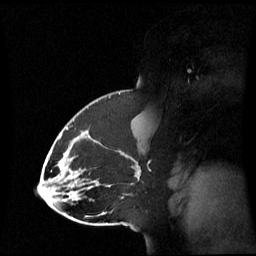
Breast MRI (dynamic contrast-enhanced), one sagittal slice; slice 38 of 60 in the series (ordered by position); dynamic contrast-enhanced series, image 2 of 3 at this slice position (ordered by acquisition); 1.5 T; TE 4.2 ms, TR 8.4 ms; 2.8 mm slice thickness; 256 × 256 image matrix, field of view 270 × 270 mm. Patient: female, 43 years. From the clinical record (not read from this slice): setting: breast cancer imaged before/during neoadjuvant chemotherapy; receptor status: triple-negative.
Structures marked on this image (semi-automatic segmentation, software-assisted and operator-edited):
- analysis volume of interest (the breast-tissue region the enhancement analysis was run in; not a lesion): bounding box [x1, y1, x2, y2] px = [65, 118, 143, 198]
- tumour enhancement mask (voxels above the 70 % enhancement threshold inside the analysis volume of interest): [66, 127, 121, 184]